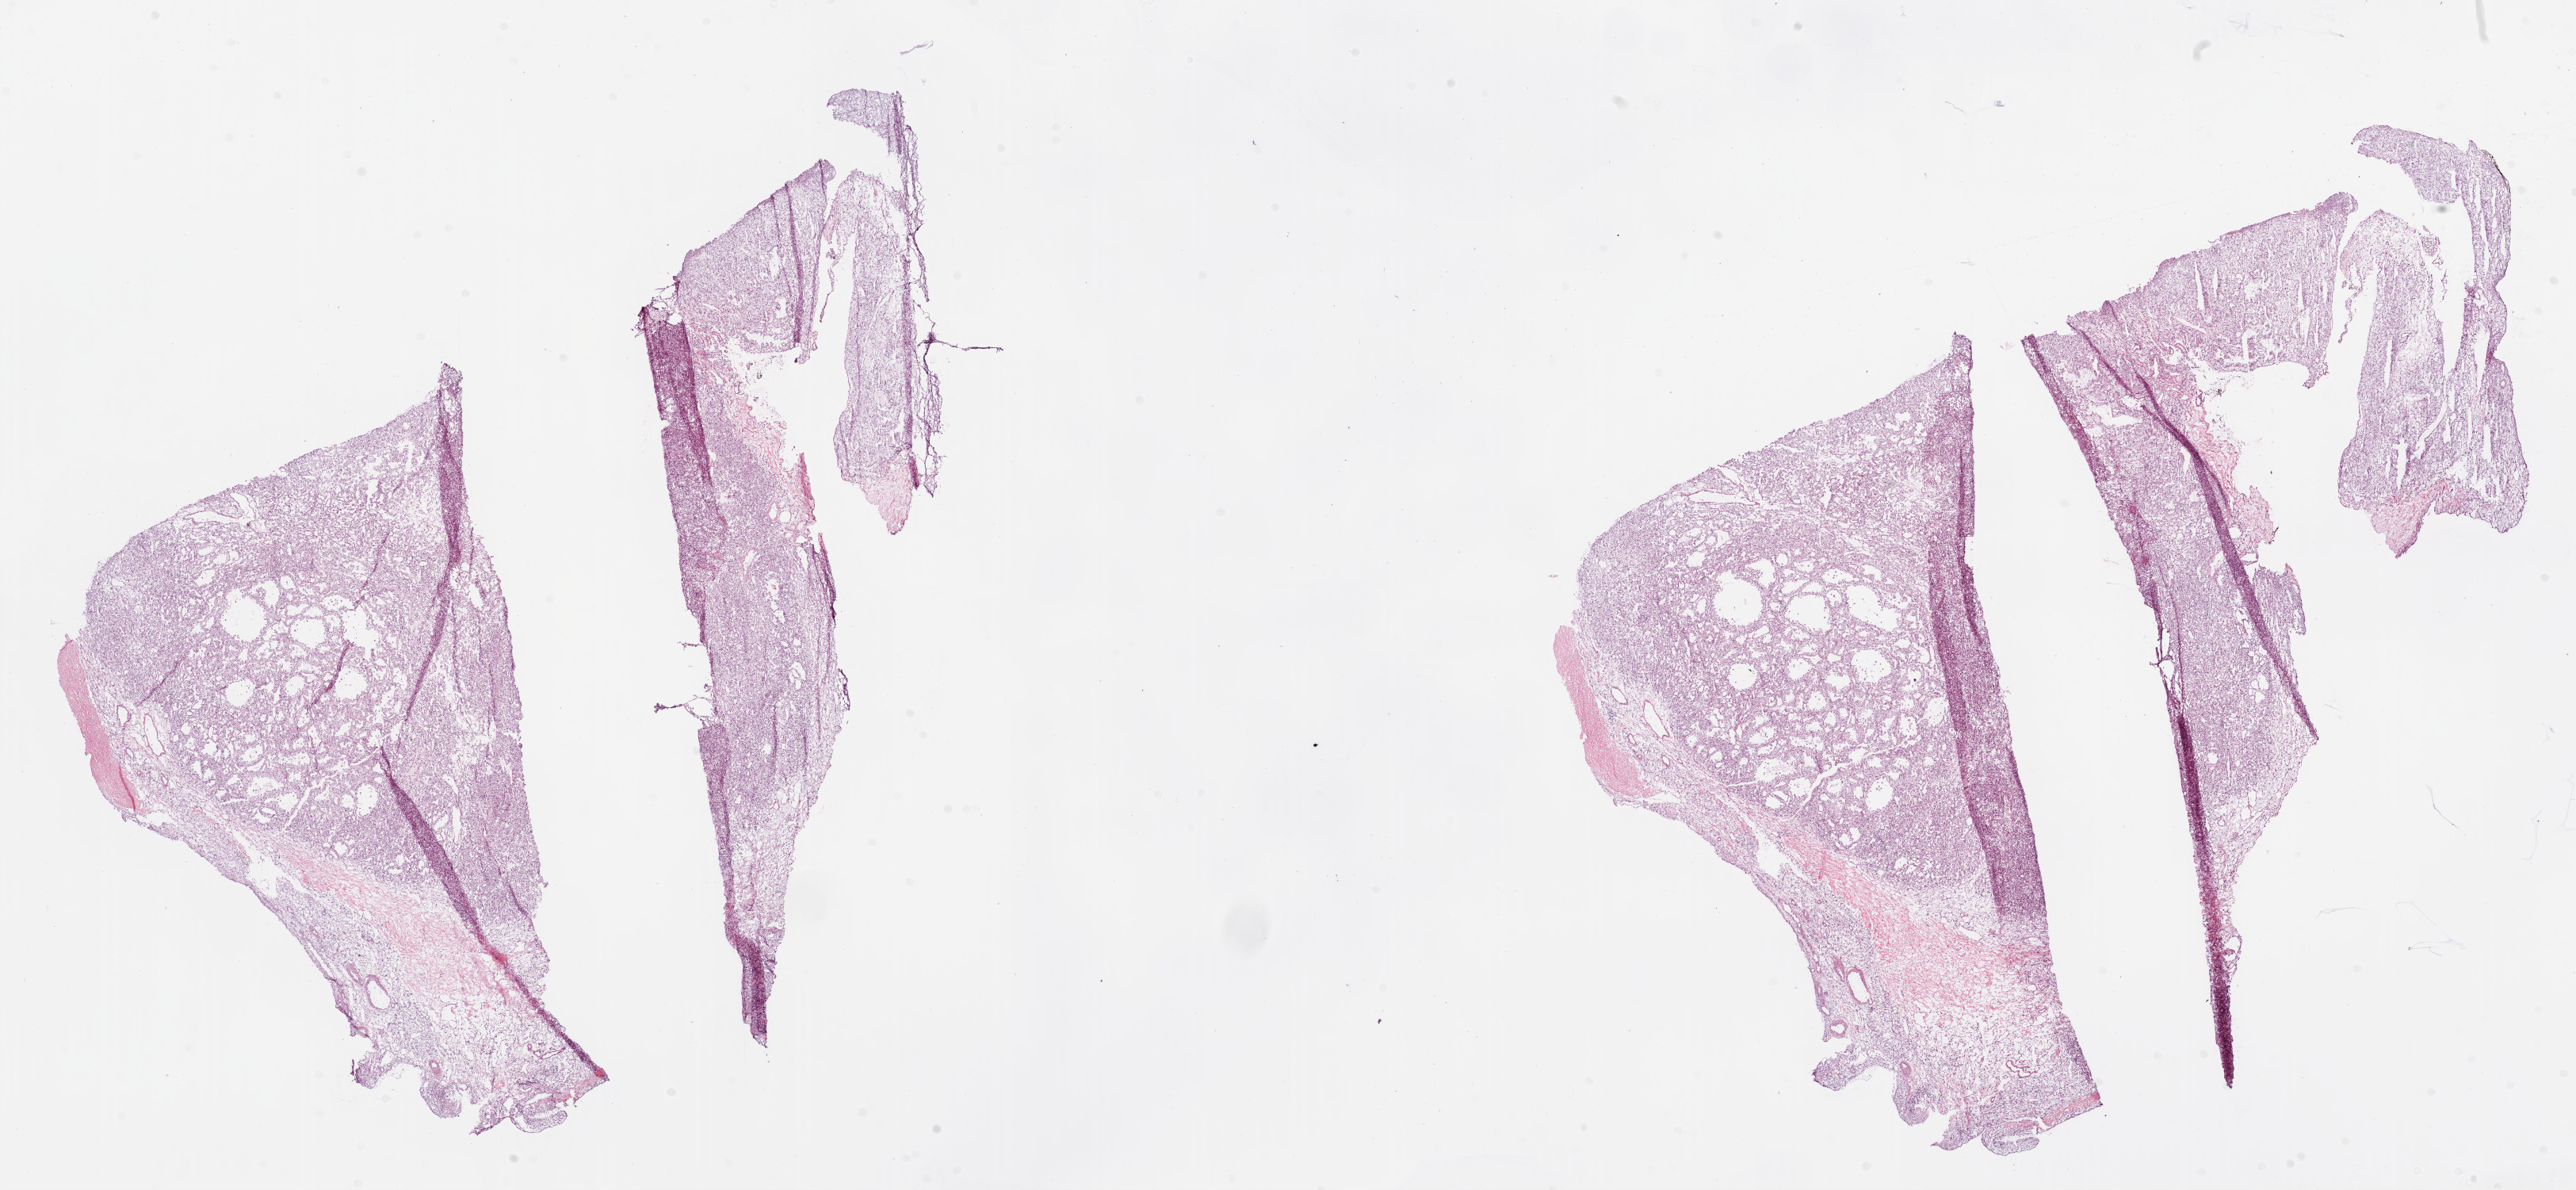
Whole-slide histology image, H&E, shown as a low-resolution overview of the whole scanned area (about 26.1 x 12.0 mm, from a 20x scan), frozen section from the bottom of the tissue portion, sample: primary tumour, kidney. Male patient; age at initial diagnosis 46 years. Histologic grade: G2 (moderately differentiated). Composition of this section per pathologist review: tumour cells 80%, tumour nuclei 80%, normal cells 0%, stromal cells 20%, necrosis 0%.
* pathologic diagnosis: Clear cell adenocarcinoma, NOS
* AJCC pathologic stage: I